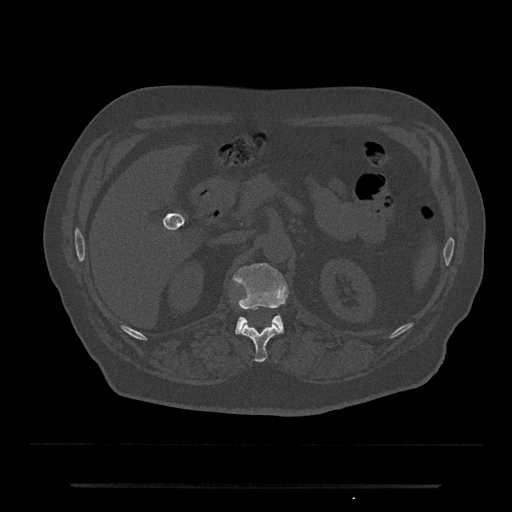
CT including the spine, one axial slice; slice 566 of 797 in the series (ordered by position); reconstruction kernel Br40s/3; 120 kVp; bone window (W 1800 / L 400 HU); 0.5 mm slice thickness; 512 × 512 image matrix, field of view 434 × 434 mm. Patient: male, 80 years. Case-level facts recorded for this patient, not image findings: primary cancer: prostate.
Structures marked on this image (semi-automatically segmented with operator editing):
- L1 vertebra: bounding box <233,263,288,334> (left, top, right, bottom; pixels)
- T12 vertebra: <242,324,281,362>